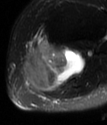
MRI of an extremity soft-tissue mass, one axial slice. Position 45 of 78 along the scan axis. T2-weighted fat-saturated. MR volume resampled by the dataset authors to the PET/CT grid (not the native acquisition matrix). 3.27 mm slice thickness. 107 × 125 image matrix, field of view 104 × 122 mm. Female patient. From the clinical record (not read from this slice): histological type: extraskeletal high grade osteogenic sarcoma; grade: high; site of the primary tumour: left calf.
Outlined on this slice (expert contour drawn on MRI and transferred to this co-registered scan by the dataset authors):
- gross tumour volume (mass): bounding box <23,43,86,92> (left, top, right, bottom; pixels)